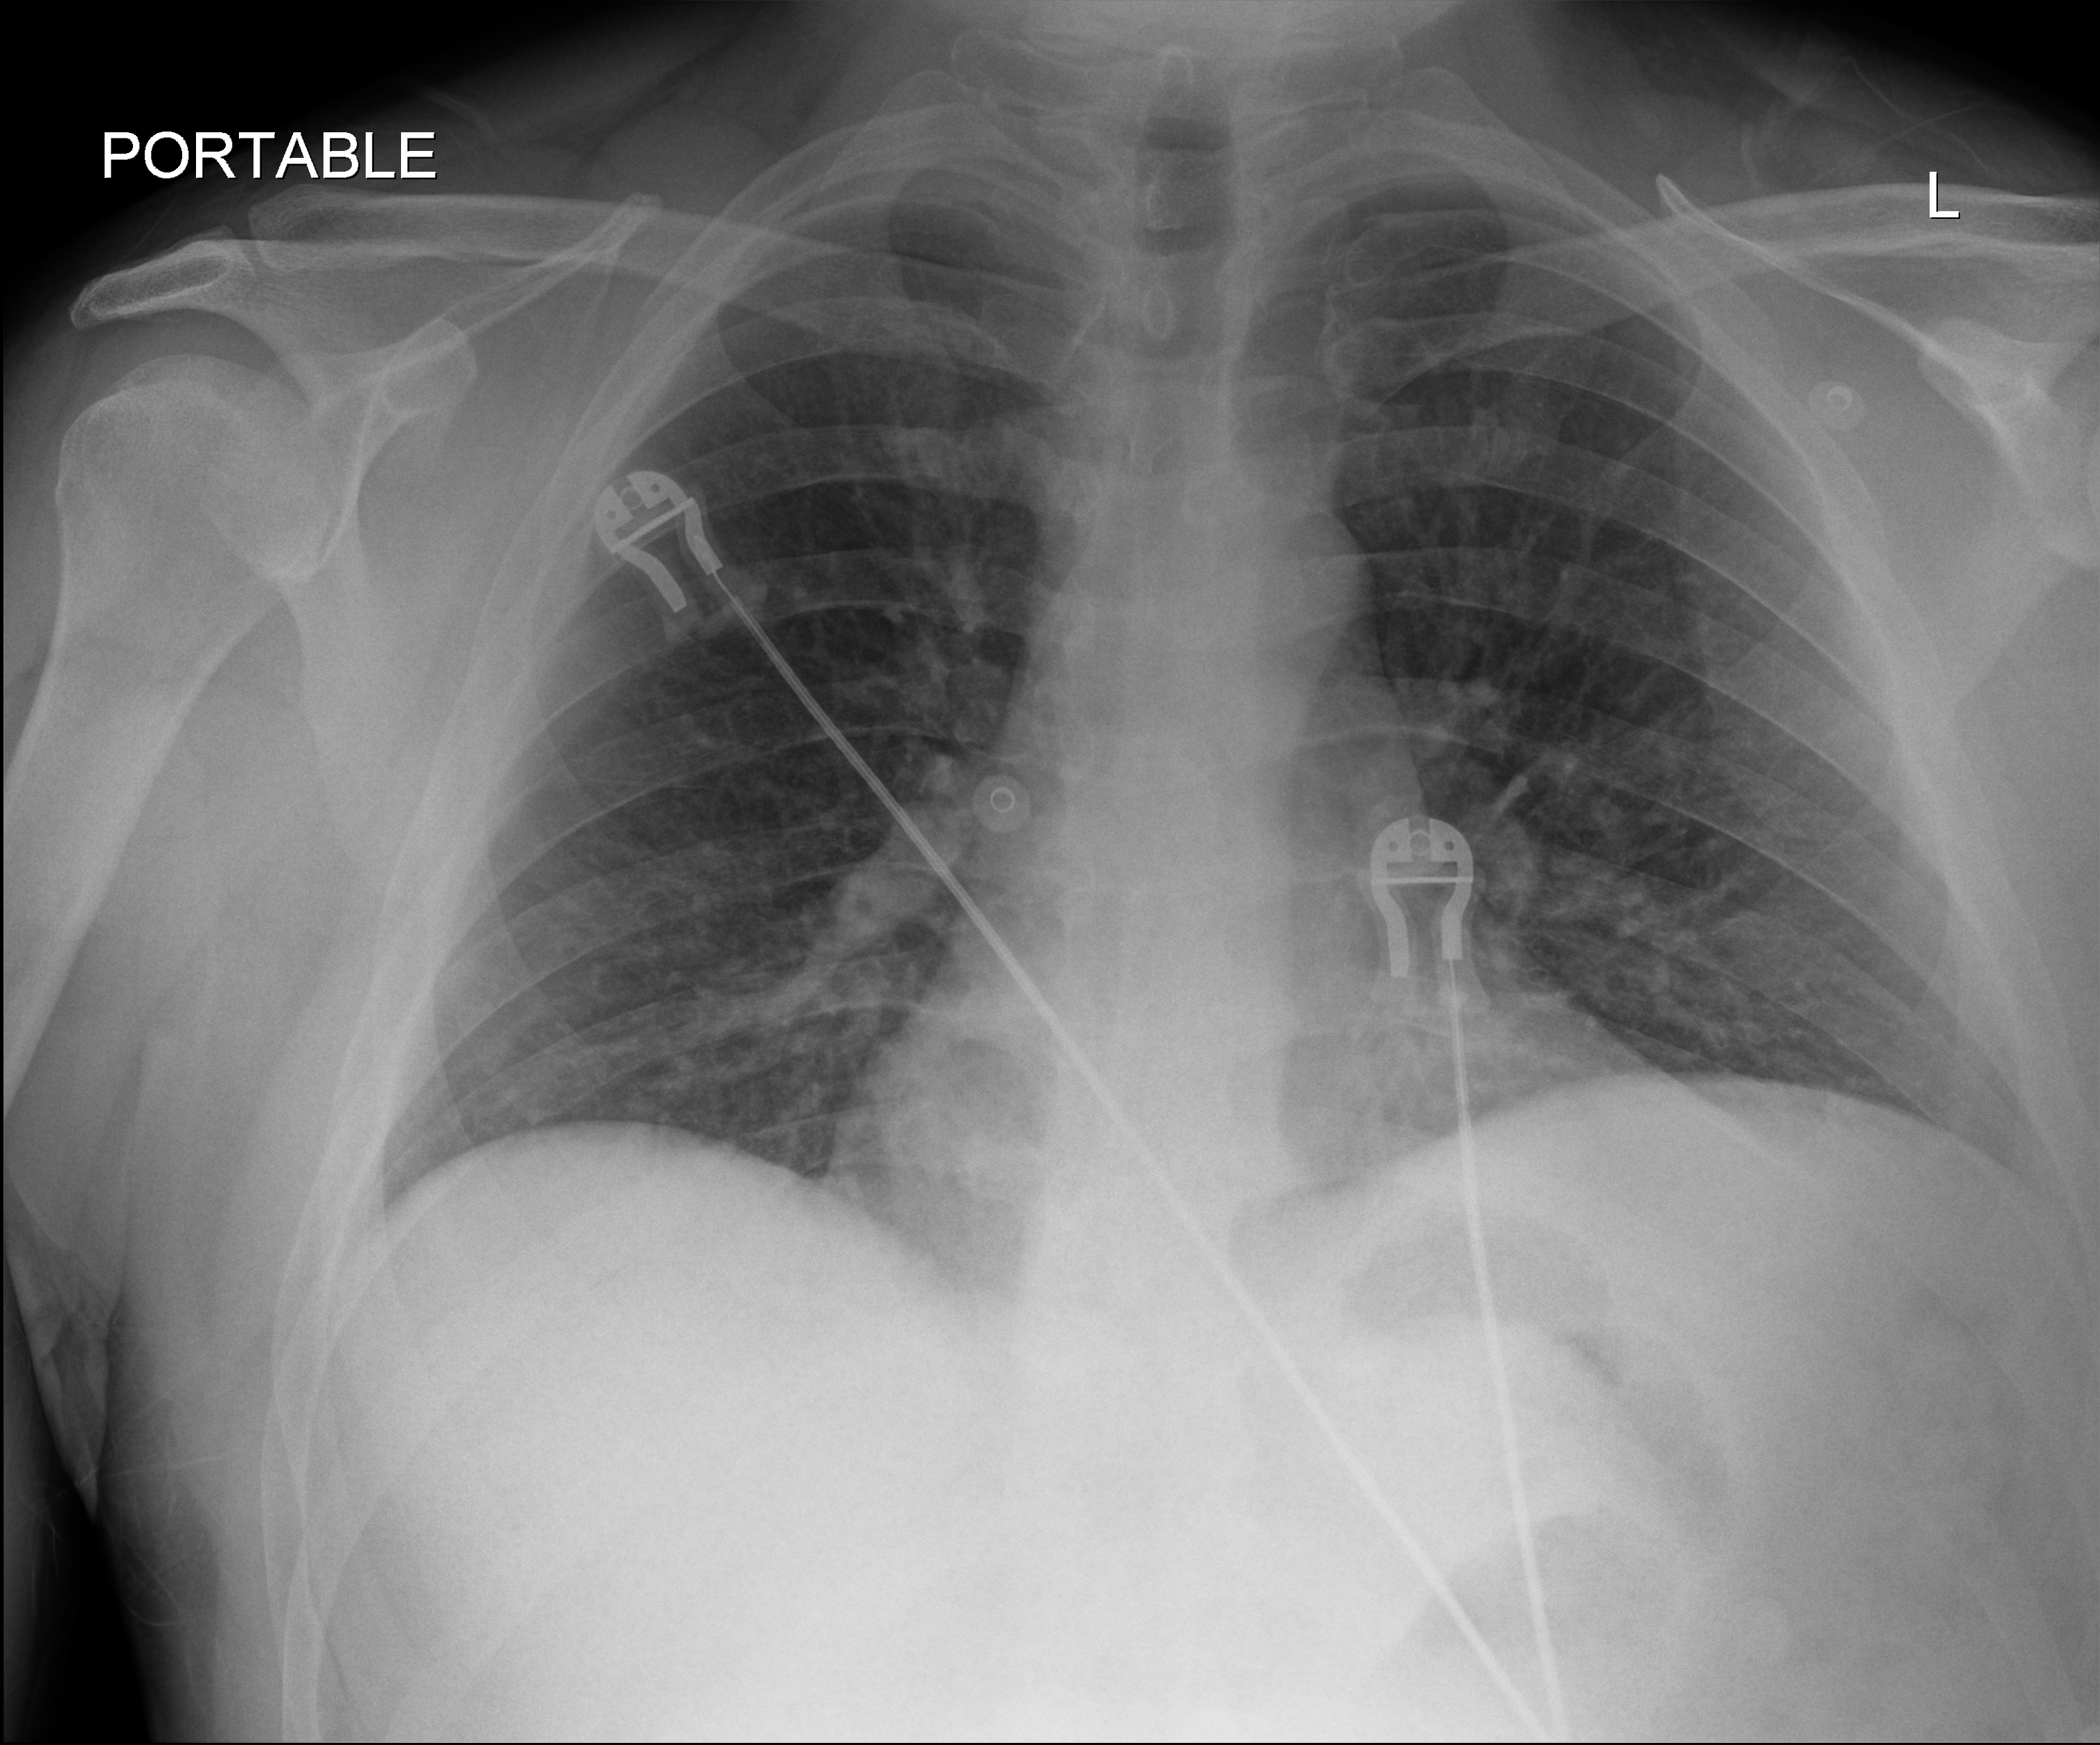
Chest radiograph, anteroposterior (AP) projection. Patient hospitalised with COVID-19; male, aged 18–59 years.
From the hospital-stay record, not from the radiograph (when in the stay this image was taken is not recorded):
- admitted to intensive care during this hospital stay: no
- hypertension (admission record): yes